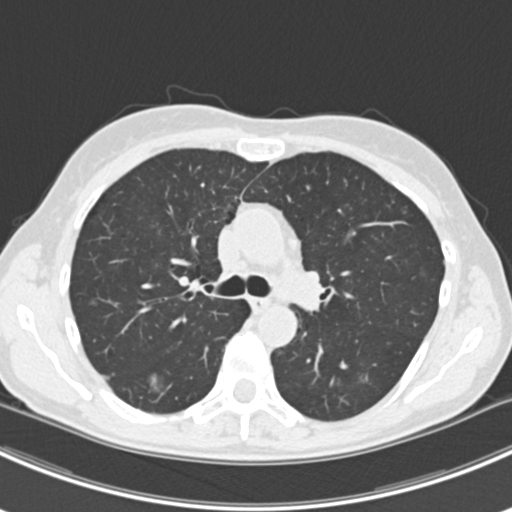
Axial slice from a low-dose chest CT screening exam, baseline screening round, lung window (W 1500 / L -600 HU), 2 mm slice thickness, standard (soft-tissue) reconstruction kernel (B30f), slice 65 of 224 in the series. Female, age 63 years at enrolment. Current smoker at enrolment.
2 lesions marked by an expert reader on this slice (largest first), bounding box <135,365,178,402> (left, top, right, bottom; pixels); <345,361,387,395>. The screening reader recorded 10 non-calcified nodules or masses ≥4 mm on this exam (right lower lobe, right lower lobe, left lower lobe, left lower lobe, right middle lobe, right lower lobe, left lower lobe, left upper lobe, right upper lobe, left upper lobe); which of them these boxes mark is not recorded. Participant outcome: lung cancer diagnosed 751 days after this screen (after the third annual screen) — bronchiolo-alveolar adenocarcinoma, NOS, right upper lobe, right middle lobe, right lower lobe, left upper lobe, left lower lobe, moderately differentiated (G2), stage IV (AJCC 6th edition).